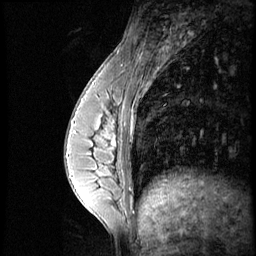
Breast MRI (dynamic contrast-enhanced), one sagittal slice; slice 19 of 56 in the series (ordered by position); dynamic contrast-enhanced series, image 2 of 4 at this slice position (ordered by acquisition); 1.5 T; TE 4.2 ms, TR 8.9 ms; 2.5 mm slice thickness; 256 × 256 image matrix. Patient: female, 35 years. From the clinical record (not read from this slice): setting: breast cancer imaged before/during neoadjuvant chemotherapy; receptor status: HER2-positive.
Annotated regions visible in this slice (semi-automatically segmented with operator editing):
- analysis volume of interest (the breast-tissue region the enhancement analysis was run in; not a lesion): bounding box (x1, y1, x2, y2) in pixels: (73, 111, 131, 164)
- tumour enhancement mask (voxels above the 140 % enhancement threshold inside the analysis volume of interest): (73, 116, 117, 149)